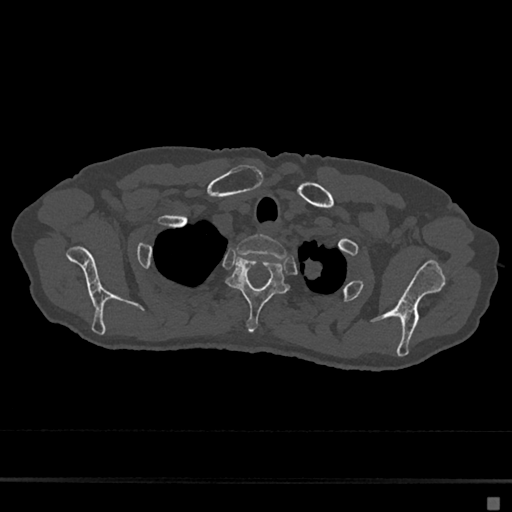
CT including the spine, one axial slice; position 578 of 797 along the scan axis; reconstruction kernel Br40s/3; 120 kVp; bone window (W 1800 / L 400 HU); 0.5 mm slice thickness; 512 × 512 image matrix, field of view 360 × 360 mm. Patient: female, 68 years. Case-level facts recorded for this patient, not image findings: primary cancer: renal.
Outlined on this slice (semi-automatically segmented with operator editing):
- T1 vertebra: box from (x=236, y=234) to (x=287, y=260) px
- T2 vertebra: (x=226, y=255)–(x=289, y=332)